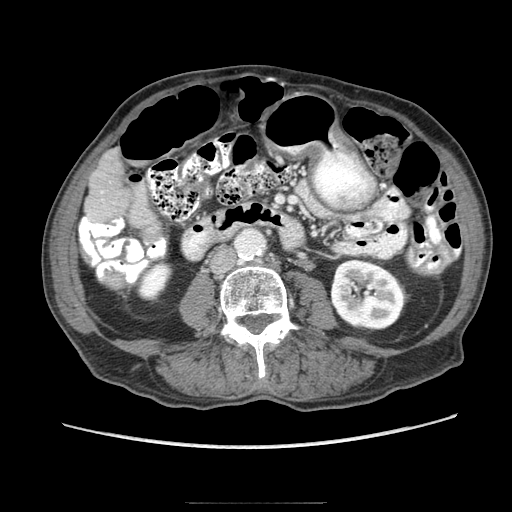
Contrast-enhanced abdominal CT (liver protocol), one axial slice. Slice 14 of 83 in the series (ordered by position). Reconstruction kernel STANDARD. 140 kVp. Soft-tissue window (W 400 / L 40 HU). 2.5 mm slice thickness. 512 × 512 image matrix, field of view 360 × 360 mm. Case-level facts recorded for this patient, not image findings: diagnosis: hepatocellular carcinoma (patient treated with transarterial chemoembolisation; whether this scan precedes or follows treatment is not stated here); TNM stage (as recorded): Stage-I; Child-Pugh class: A; tumour nodularity: uninodular.
Annotated regions visible in this slice (semi-automatic segmentation, software-assisted and operator-edited):
- liver parenchyma outside the tumour (the mass and vessels are separate outlines, so this box may not span the whole liver): box from (x=84, y=148) to (x=130, y=222) px
- liver vessels: (x=85, y=192)–(x=103, y=221)